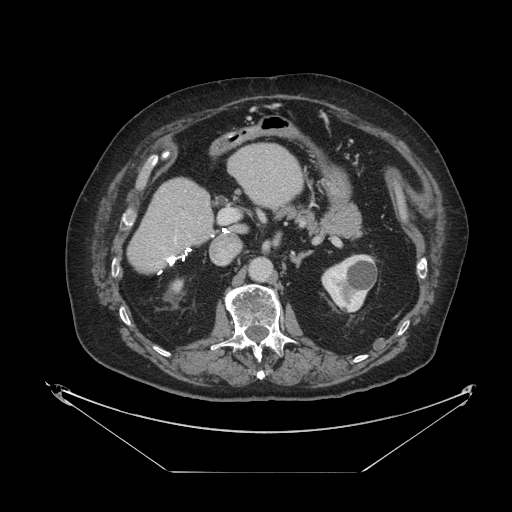
Contrast-enhanced abdominal CT, one axial slice; position 49 of 121 along the scan axis; reconstruction kernel STANDARD; 120 kVp; intravenous contrast given; soft-tissue window (W 400 / L 40 HU); 512 × 512 image matrix, field of view 500 × 500 mm. Male patient, age 68 years. From the clinical record (not read from this slice): diagnosis: colorectal cancer liver metastases, imaged before liver resection; multiple liver metastases: no; largest metastasis: 4 cm.
Annotated regions visible in this slice (expert manual segmentation):
- hepatic veins: bounding box (x1, y1, x2, y2) in pixels: (166, 237, 177, 260)
- liver: (129, 145, 303, 272)
- planned liver remnant (the part of the liver to remain after resection): (129, 145, 303, 272)
- portal vein (with intrahepatic branches): (182, 209, 237, 240)